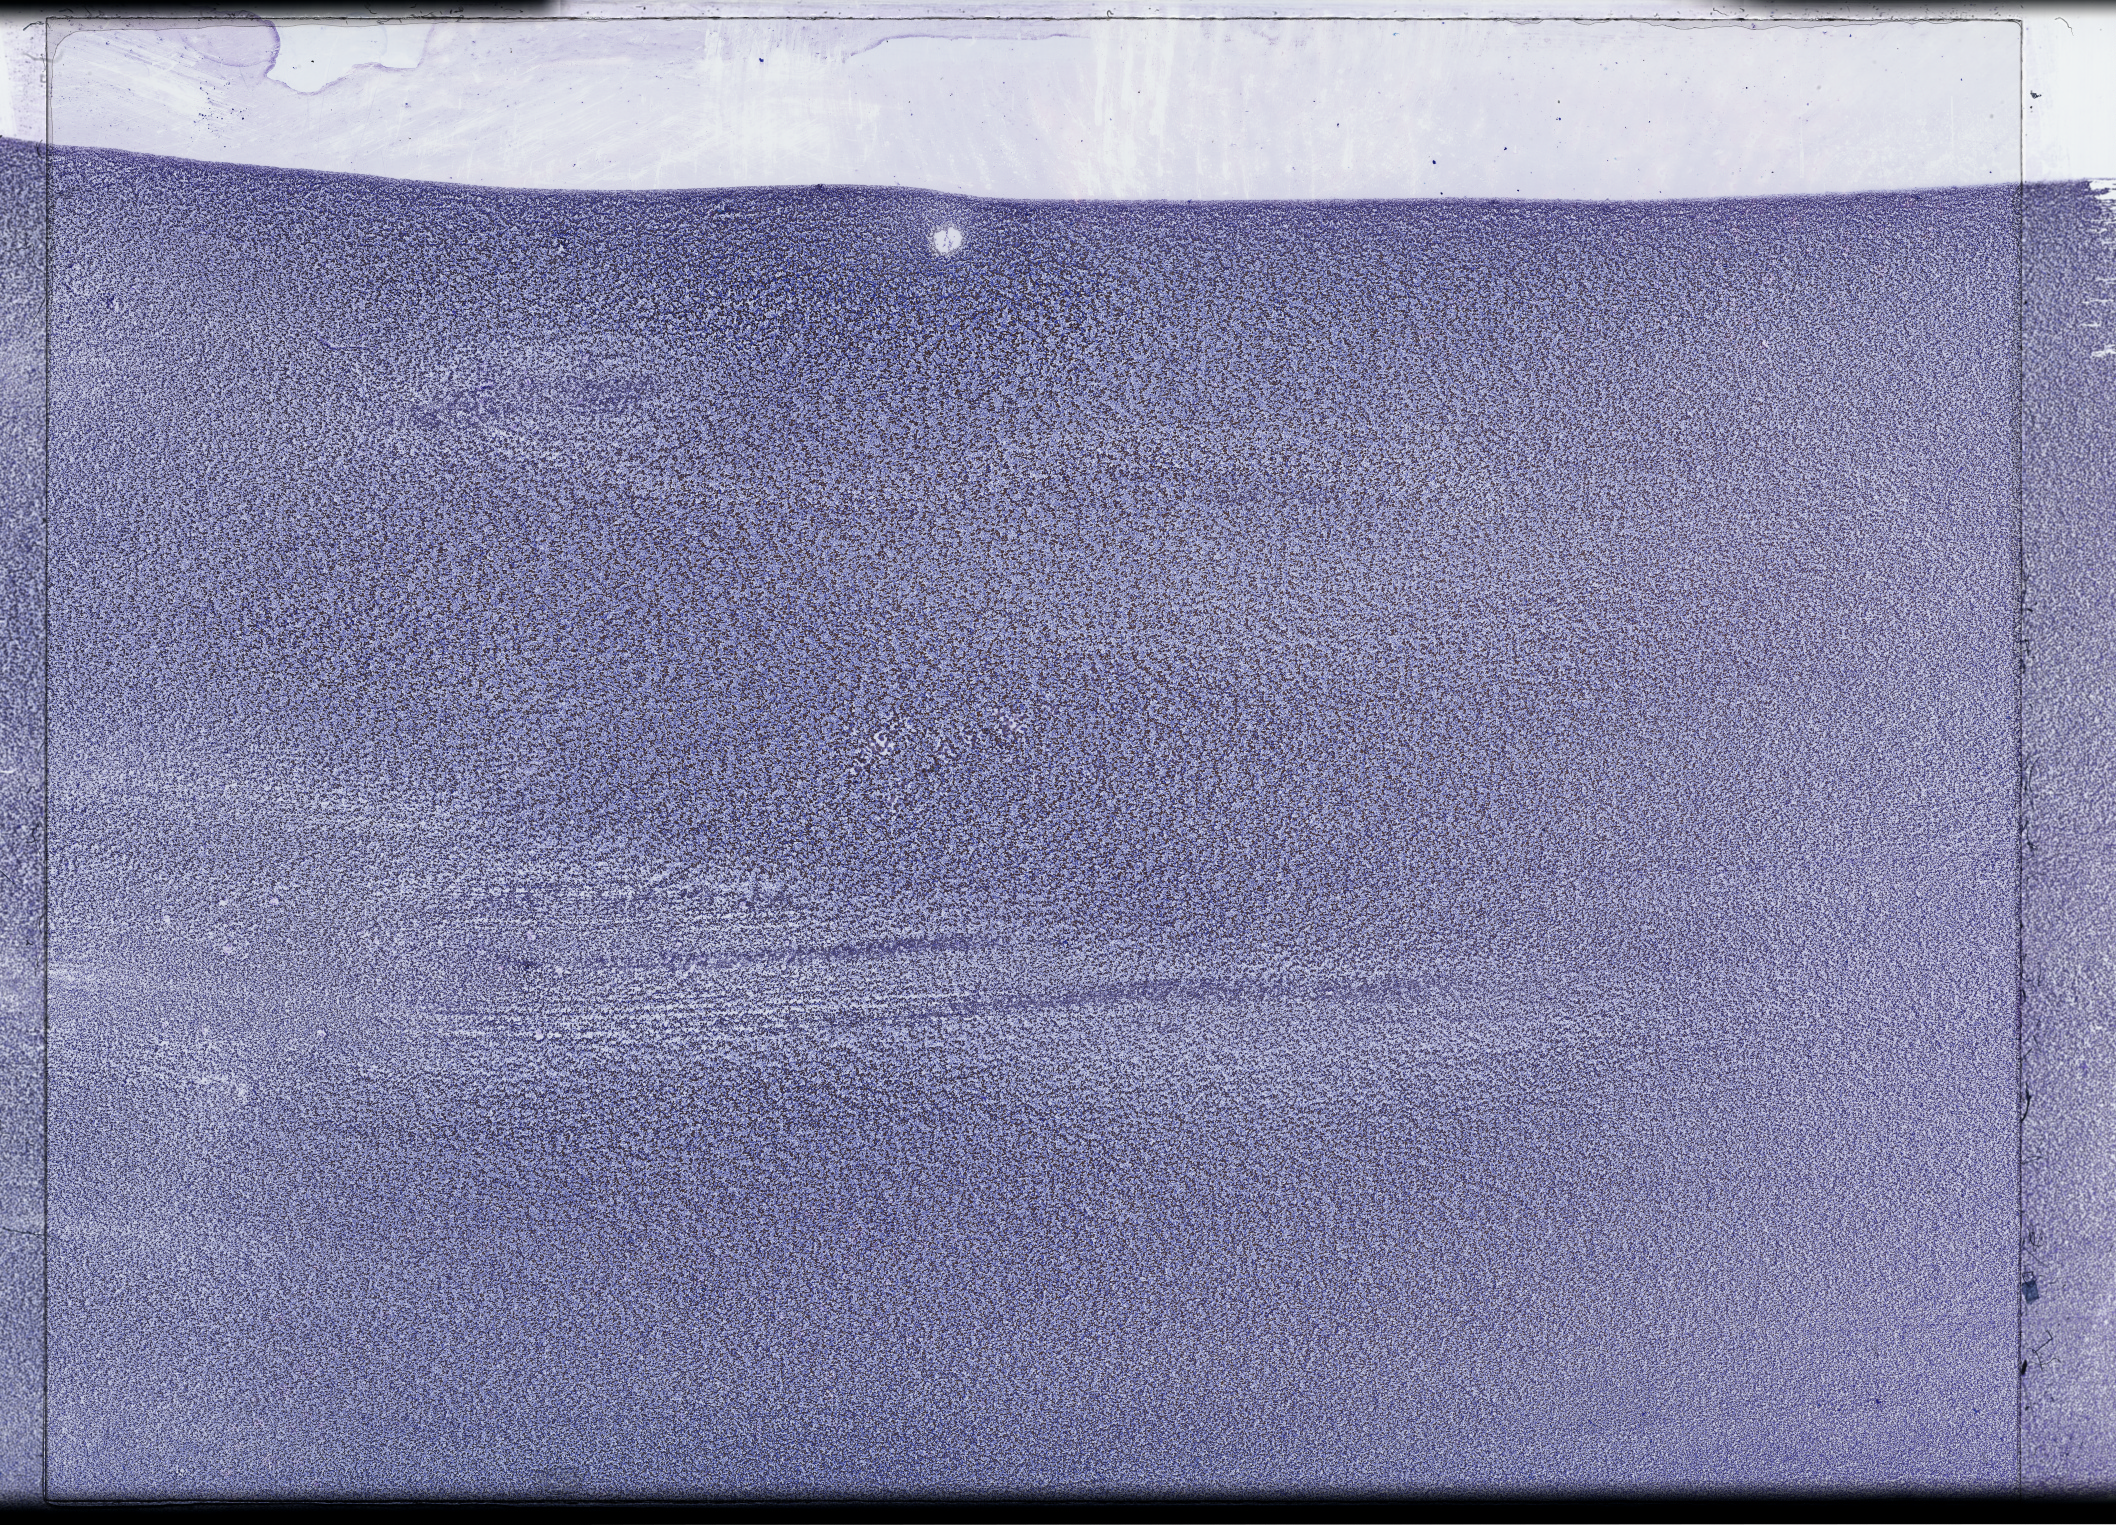
Digitized Hematoxylin and eosin (H&E) stained tissue section (whole slide), low-resolution overview of the scanned area, about 34.2 x 24.6 mm, peripheral blood (leukaemic) sample. 47-year-old male patient.
* diagnosis: Acute Myeloid Leukemia
* FAB classification: M4